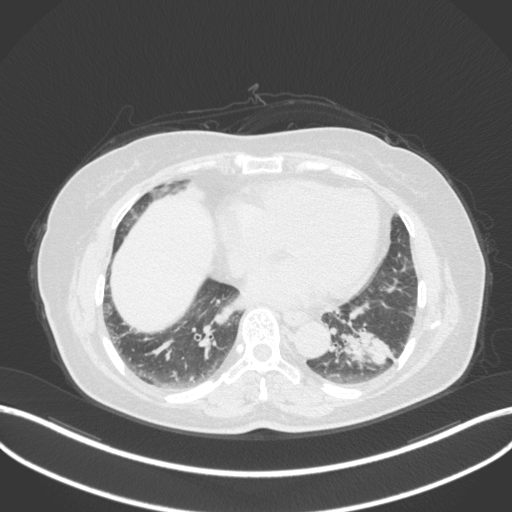
Chest CT, one axial slice. Slice 138 of 307 in the series (ordered by position). Reconstruction kernel B31f. 120 kVp. Lung window (W 1500 / L -600 HU). 512 × 512 image matrix. Patient: female, 59 years. Case-level facts recorded for this patient, not image findings: clinical TNM (as recorded): T2a N0 M0; histopathological grade: G2-3.
Outlined on this slice (bounding box drawn by a radiologist):
- lung tumour (recorded histology: adenocarcinoma): bounding box (x1, y1, x2, y2) in pixels: (337, 327, 394, 375)